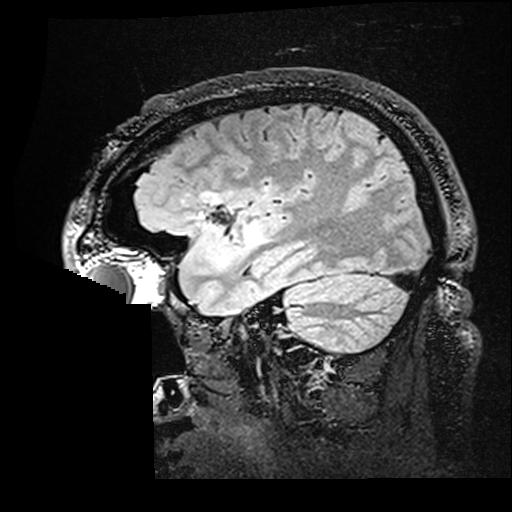
Brain MRI from a brain-tumour surgery series, one sagittal slice; position 126 of 176 along the scan axis; T2 FLAIR; 512 × 512 image matrix, field of view 250 × 250 mm. From the clinical record (not read from this slice): histopathology: Astrocytoma; WHO grade: 2; IDH mutation: yes.
Outlined on this slice (outlined manually by an expert reader):
- residual tumour: bounding box (x1, y1, x2, y2) in pixels: (202, 193, 260, 255)